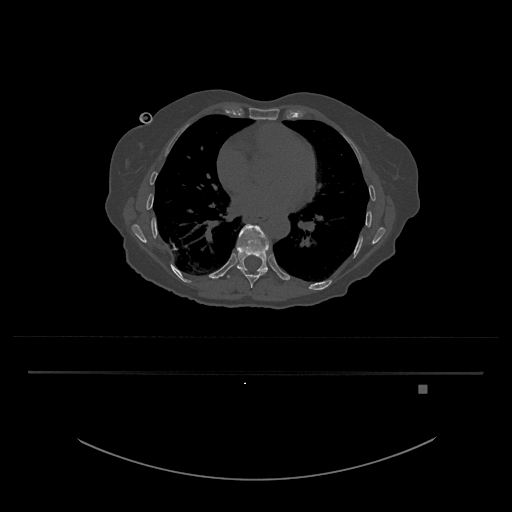
CT including the spine, one axial slice; slice 738 of 797 in the series (ordered by position); reconstruction kernel Br40s/3; bone window (W 1800 / L 400 HU); 512 × 512 image matrix, field of view 500 × 500 mm. Patient: female, 57 years. From the clinical record (not read from this slice): primary cancer: cervical.
Annotated regions visible in this slice (semi-automatically segmented with operator editing):
- T10 vertebra: bounding box <226,224,270,278> (left, top, right, bottom; pixels)
- T9 vertebra: <241,270,267,289>